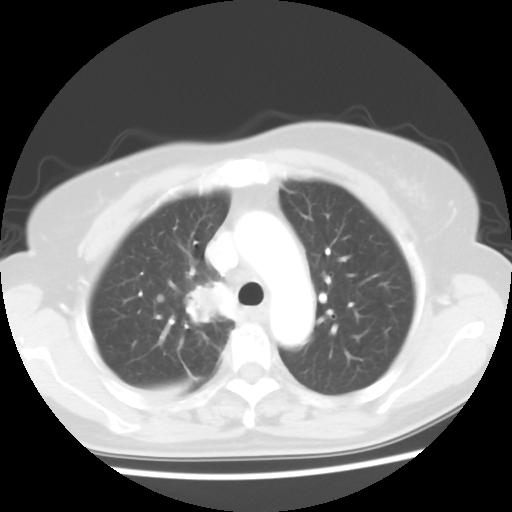
Chest CT, one axial slice; position 42 of 56 along the scan axis; reconstruction kernel STANDARD; 120 kVp; lung window (W 1500 / L -600 HU); 5 mm slice thickness; 512 × 512 image matrix. Female patient, age 62 years. From the clinical record (not read from this slice): clinical TNM (as recorded): T2 N1 M1a.
Outlined on this slice (rectangle marked by the reading radiologist):
- lung tumour (recorded histology: adenocarcinoma): bounding box <185,272,236,330> (left, top, right, bottom; pixels)